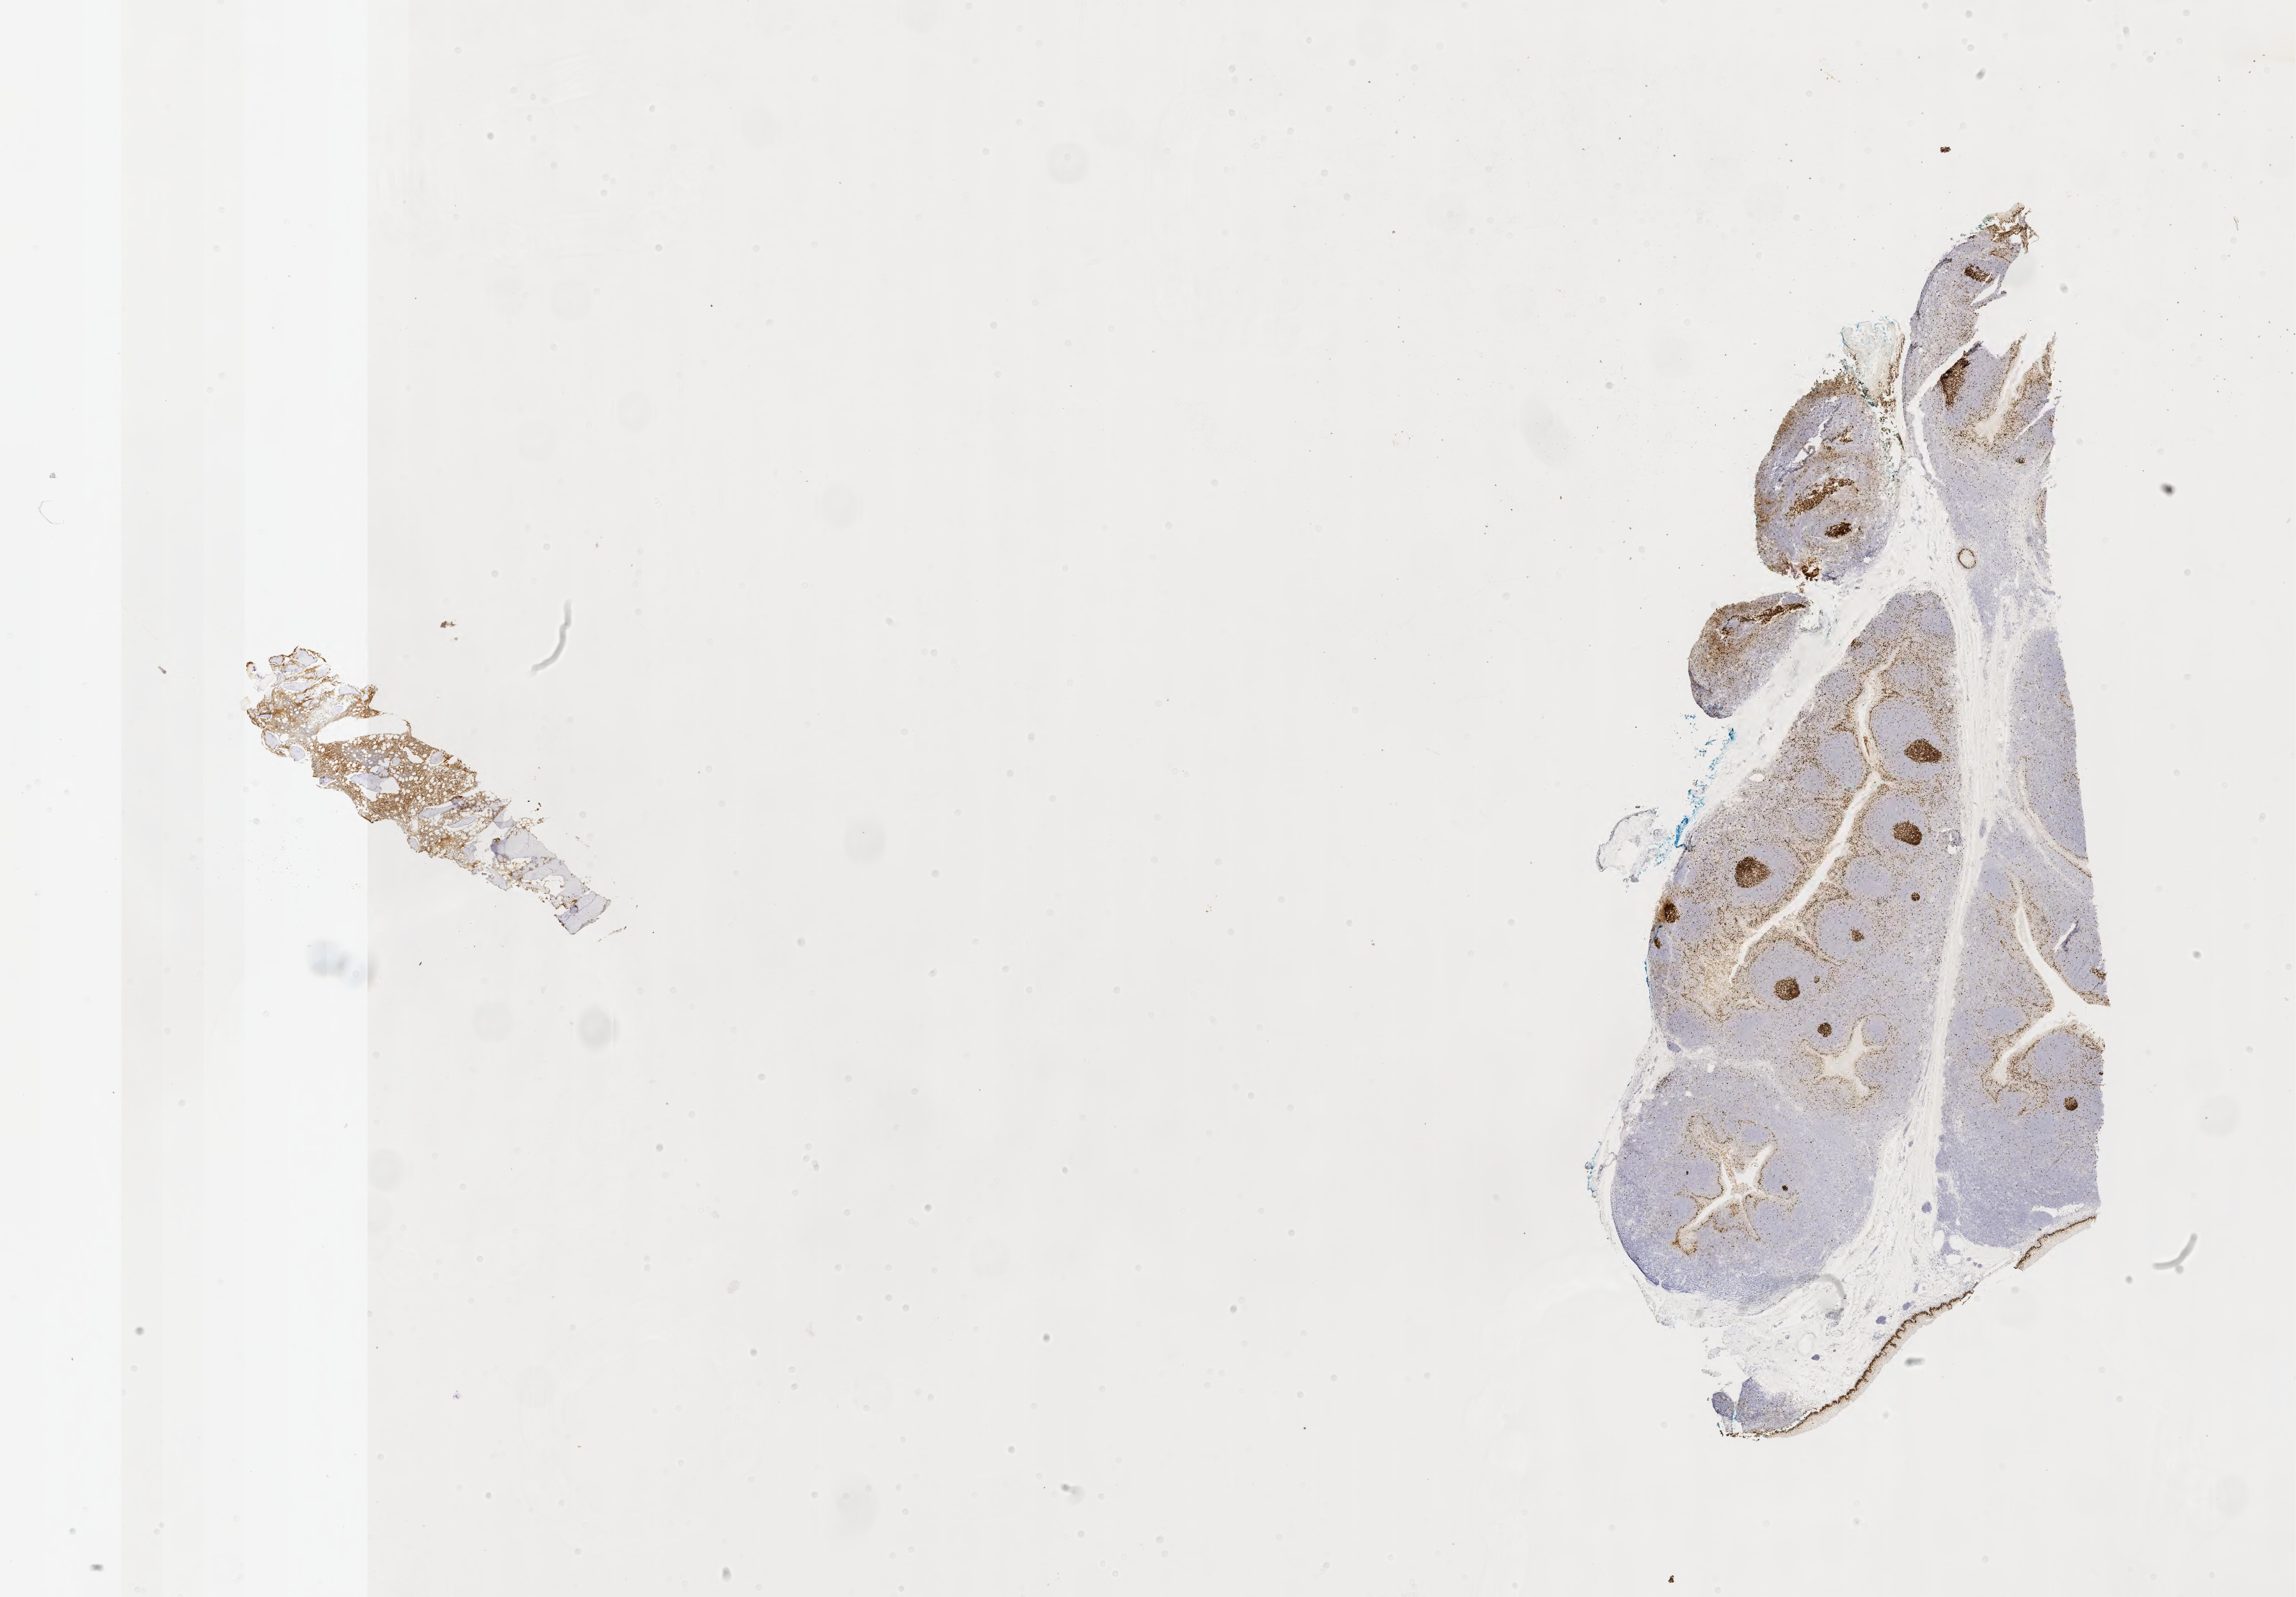
Whole-slide image, immunohistochemical stain for Ki-67 — a low-resolution overview of the entire scanned area, about 28.2 x 19.6 mm, specimen: tumor tissue, anatomic site: bone marrow. Female, age 4 years at initial diagnosis.
Diagnosis: Burkitt lymphoma, NOS.